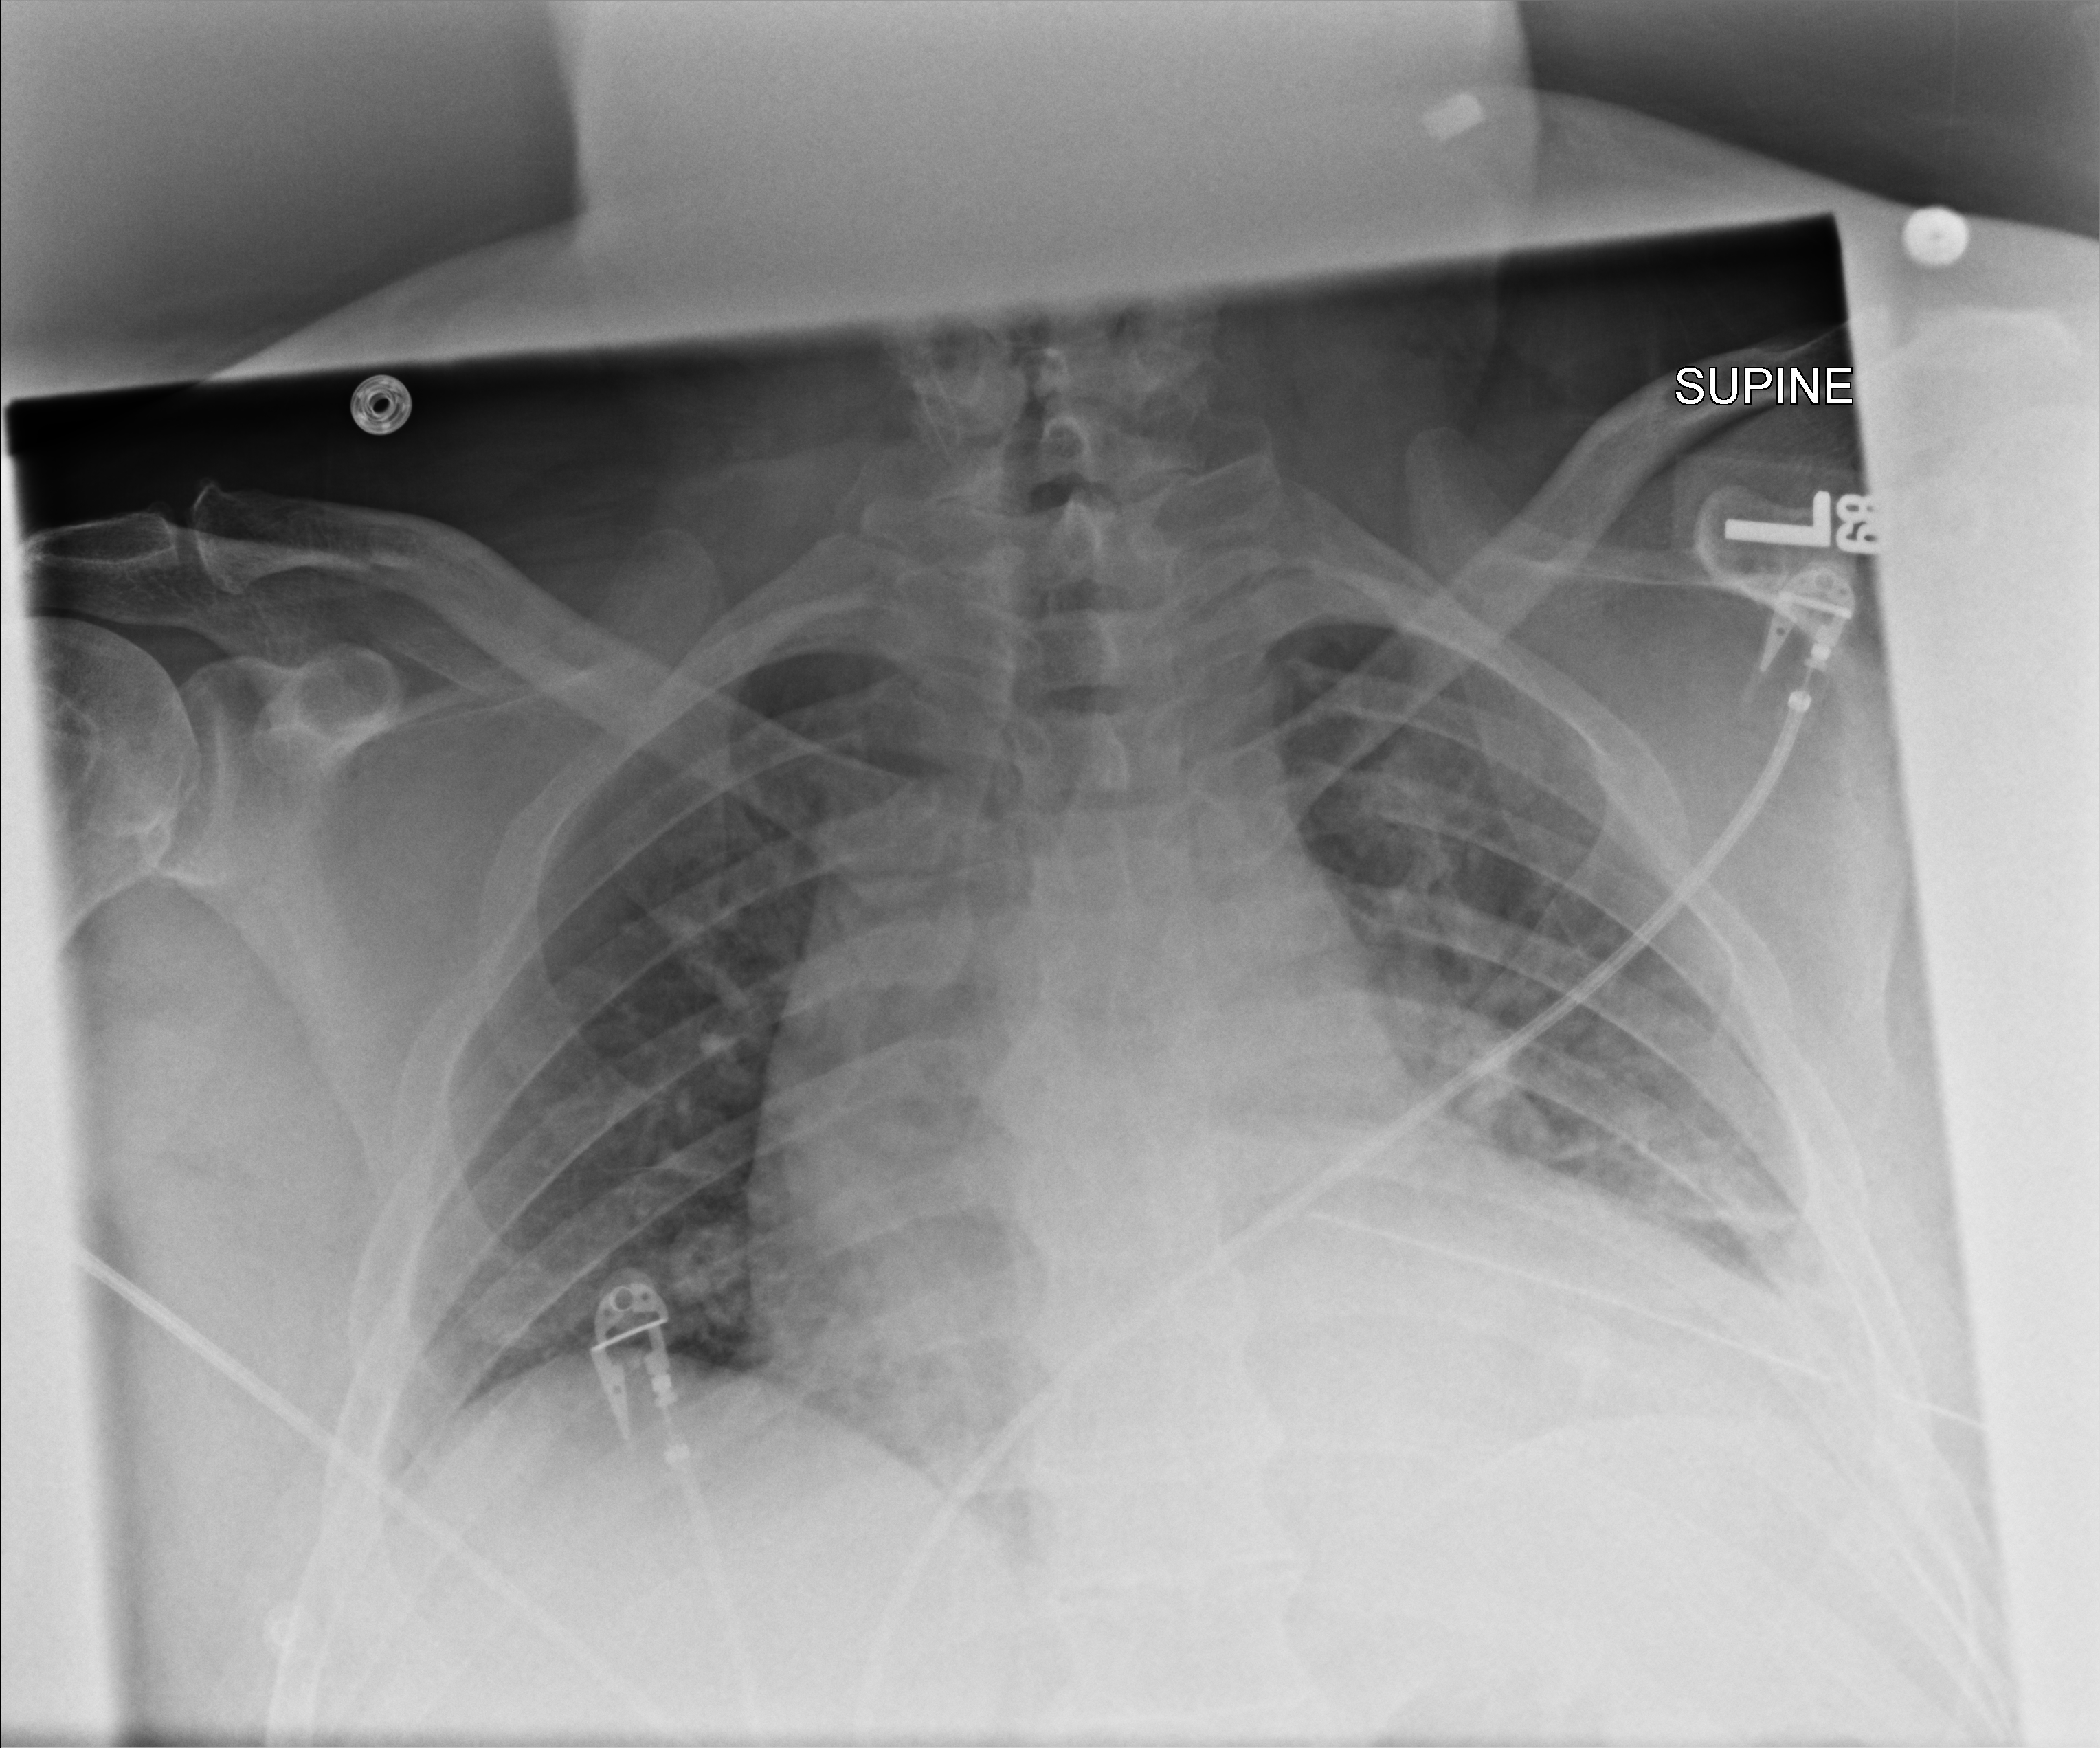
Chest X-ray (portable); anteroposterior (AP) projection. Patient hospitalised with COVID-19; male, aged 18–59 years.
Hospital-stay facts (about this admission, not read from this image; timing relative to this image not recorded):
- admitted to intensive care during this hospital stay: no
- length of hospital stay: 10 days